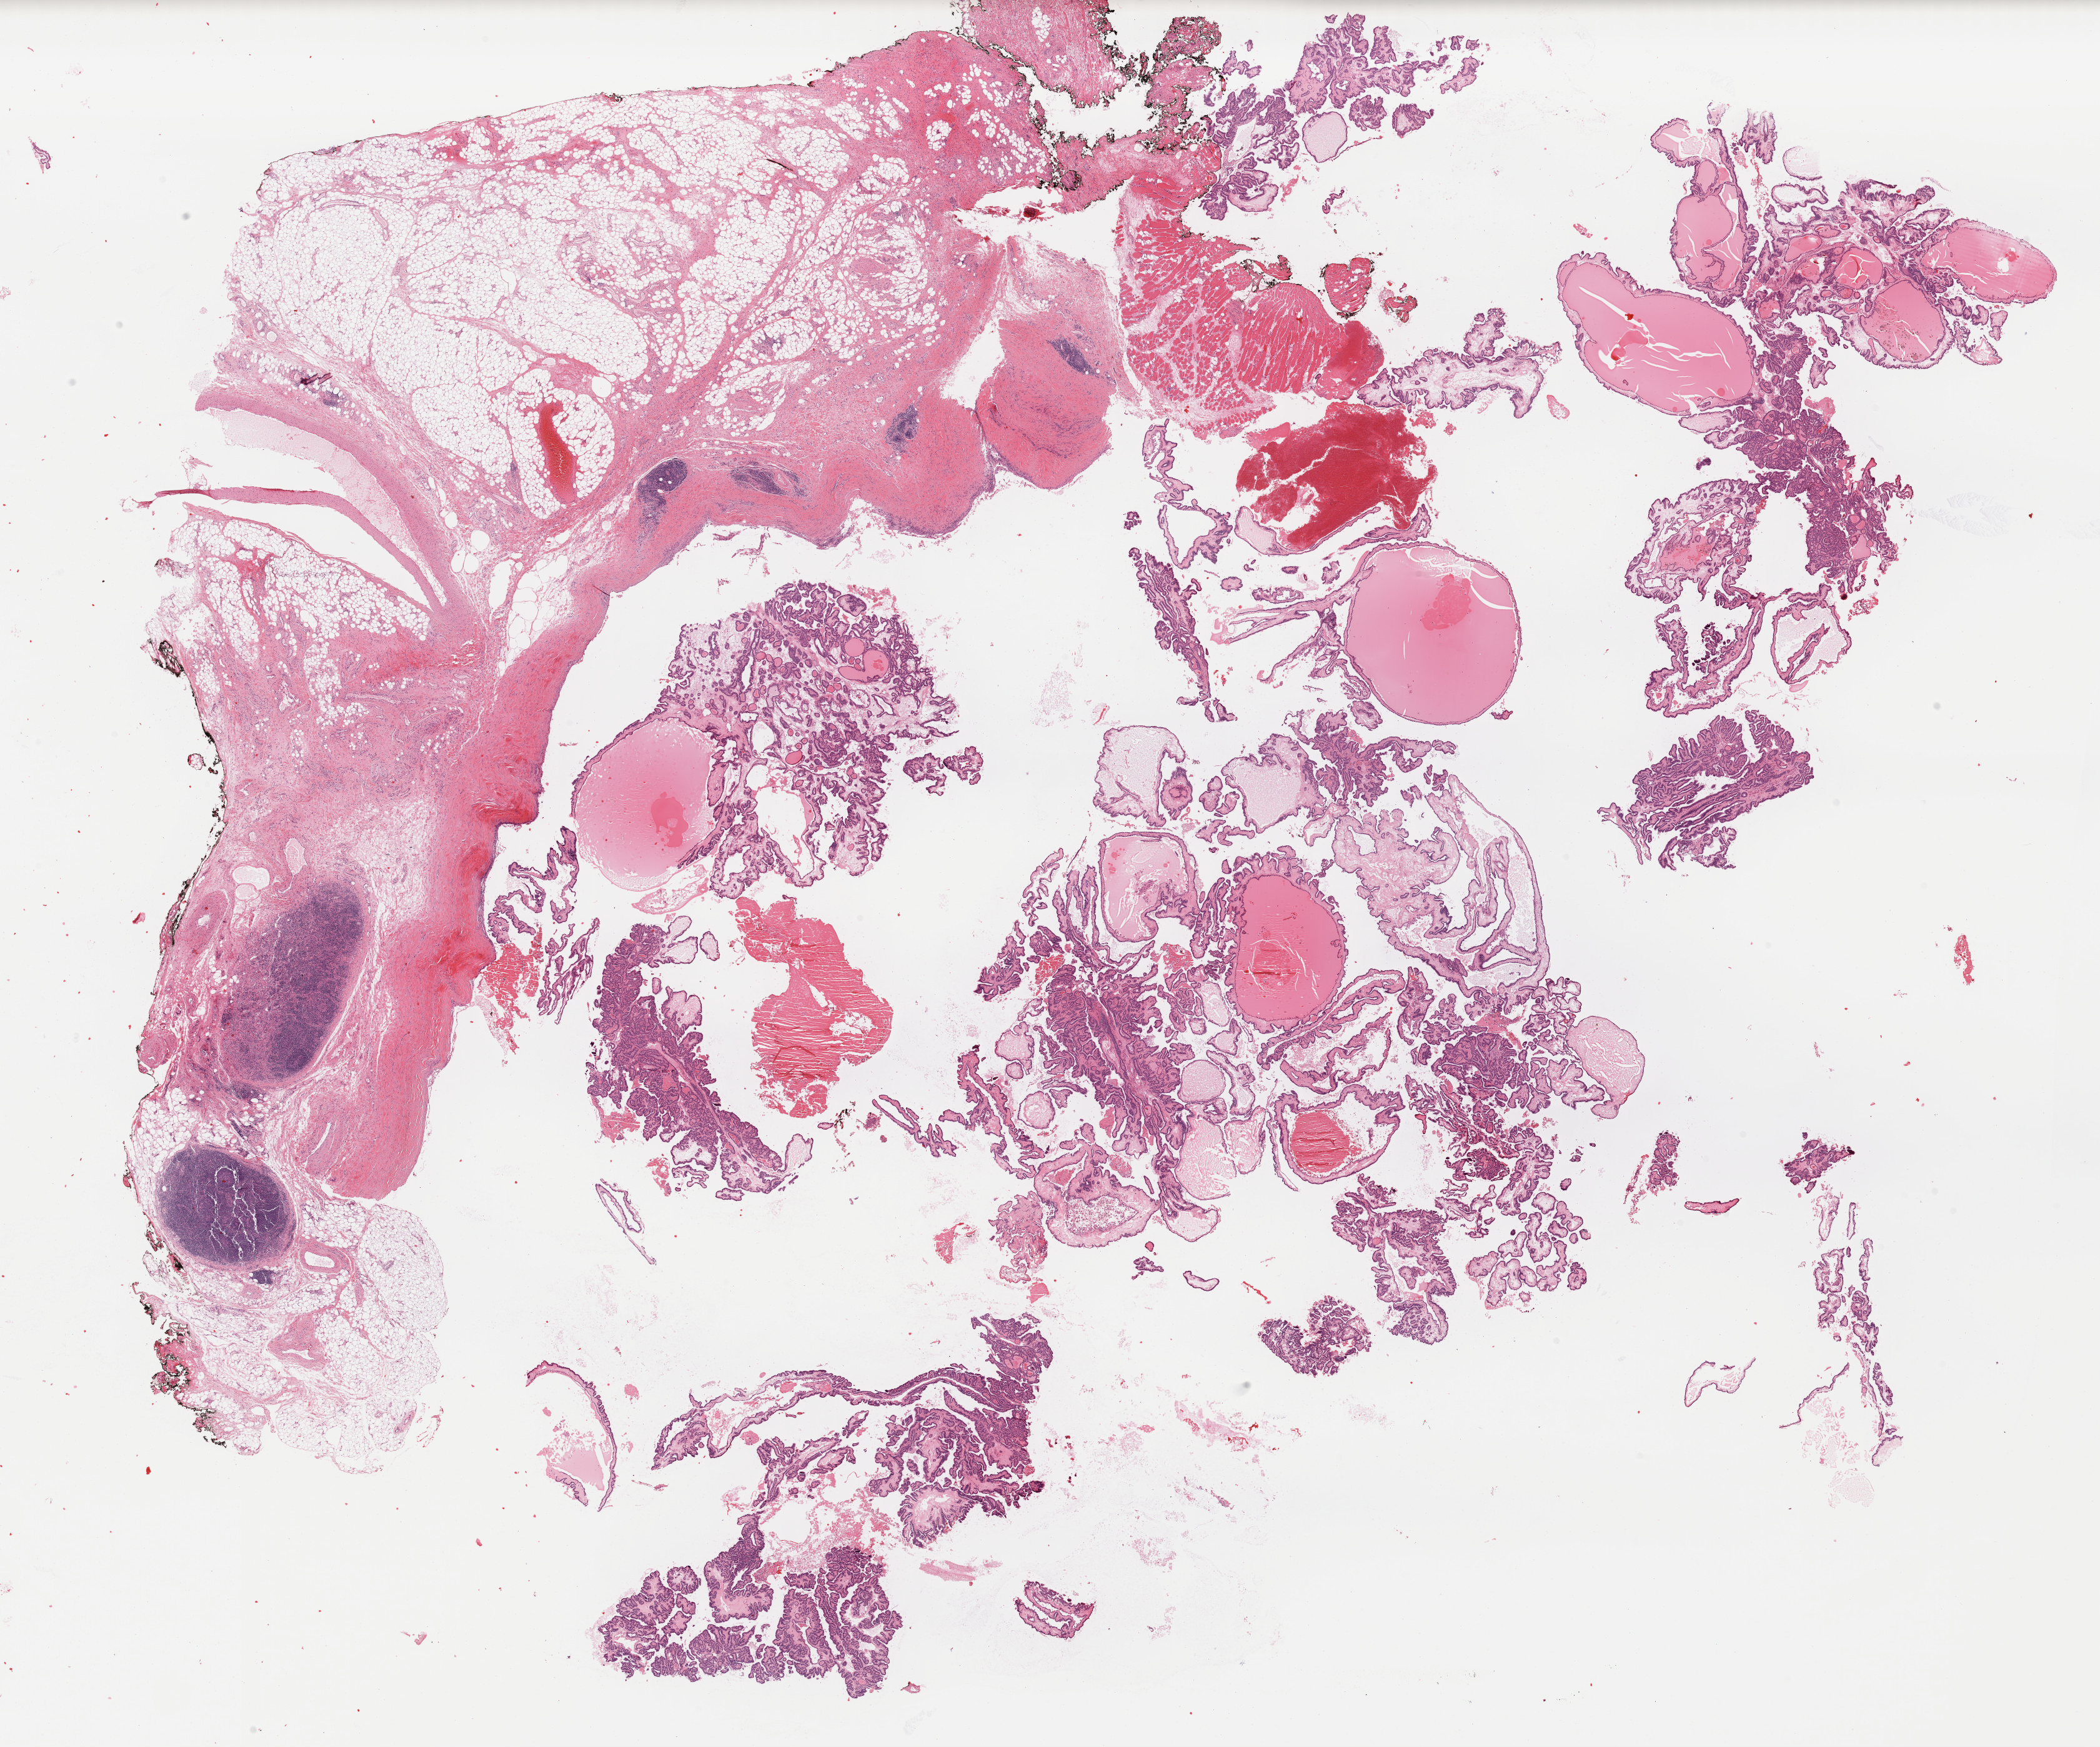
Hematoxylin and eosin (H&E) stained whole-slide image — a low-resolution overview of the entire scanned area, about 26.5 x 22.1 mm (acquisition: 40x scan), formalin-fixed paraffin-embedded (FFPE) diagnostic section, thyroid, primary tumour sample. Female, age 68 years at initial diagnosis.
- TNM: T4a N1b MX
- AJCC pathologic stage: IVA (7th edition)
- lymph nodes positive (case pathology): 13 of 40 examined
- pathologic diagnosis: Papillary adenocarcinoma, NOS (thyroid gland)